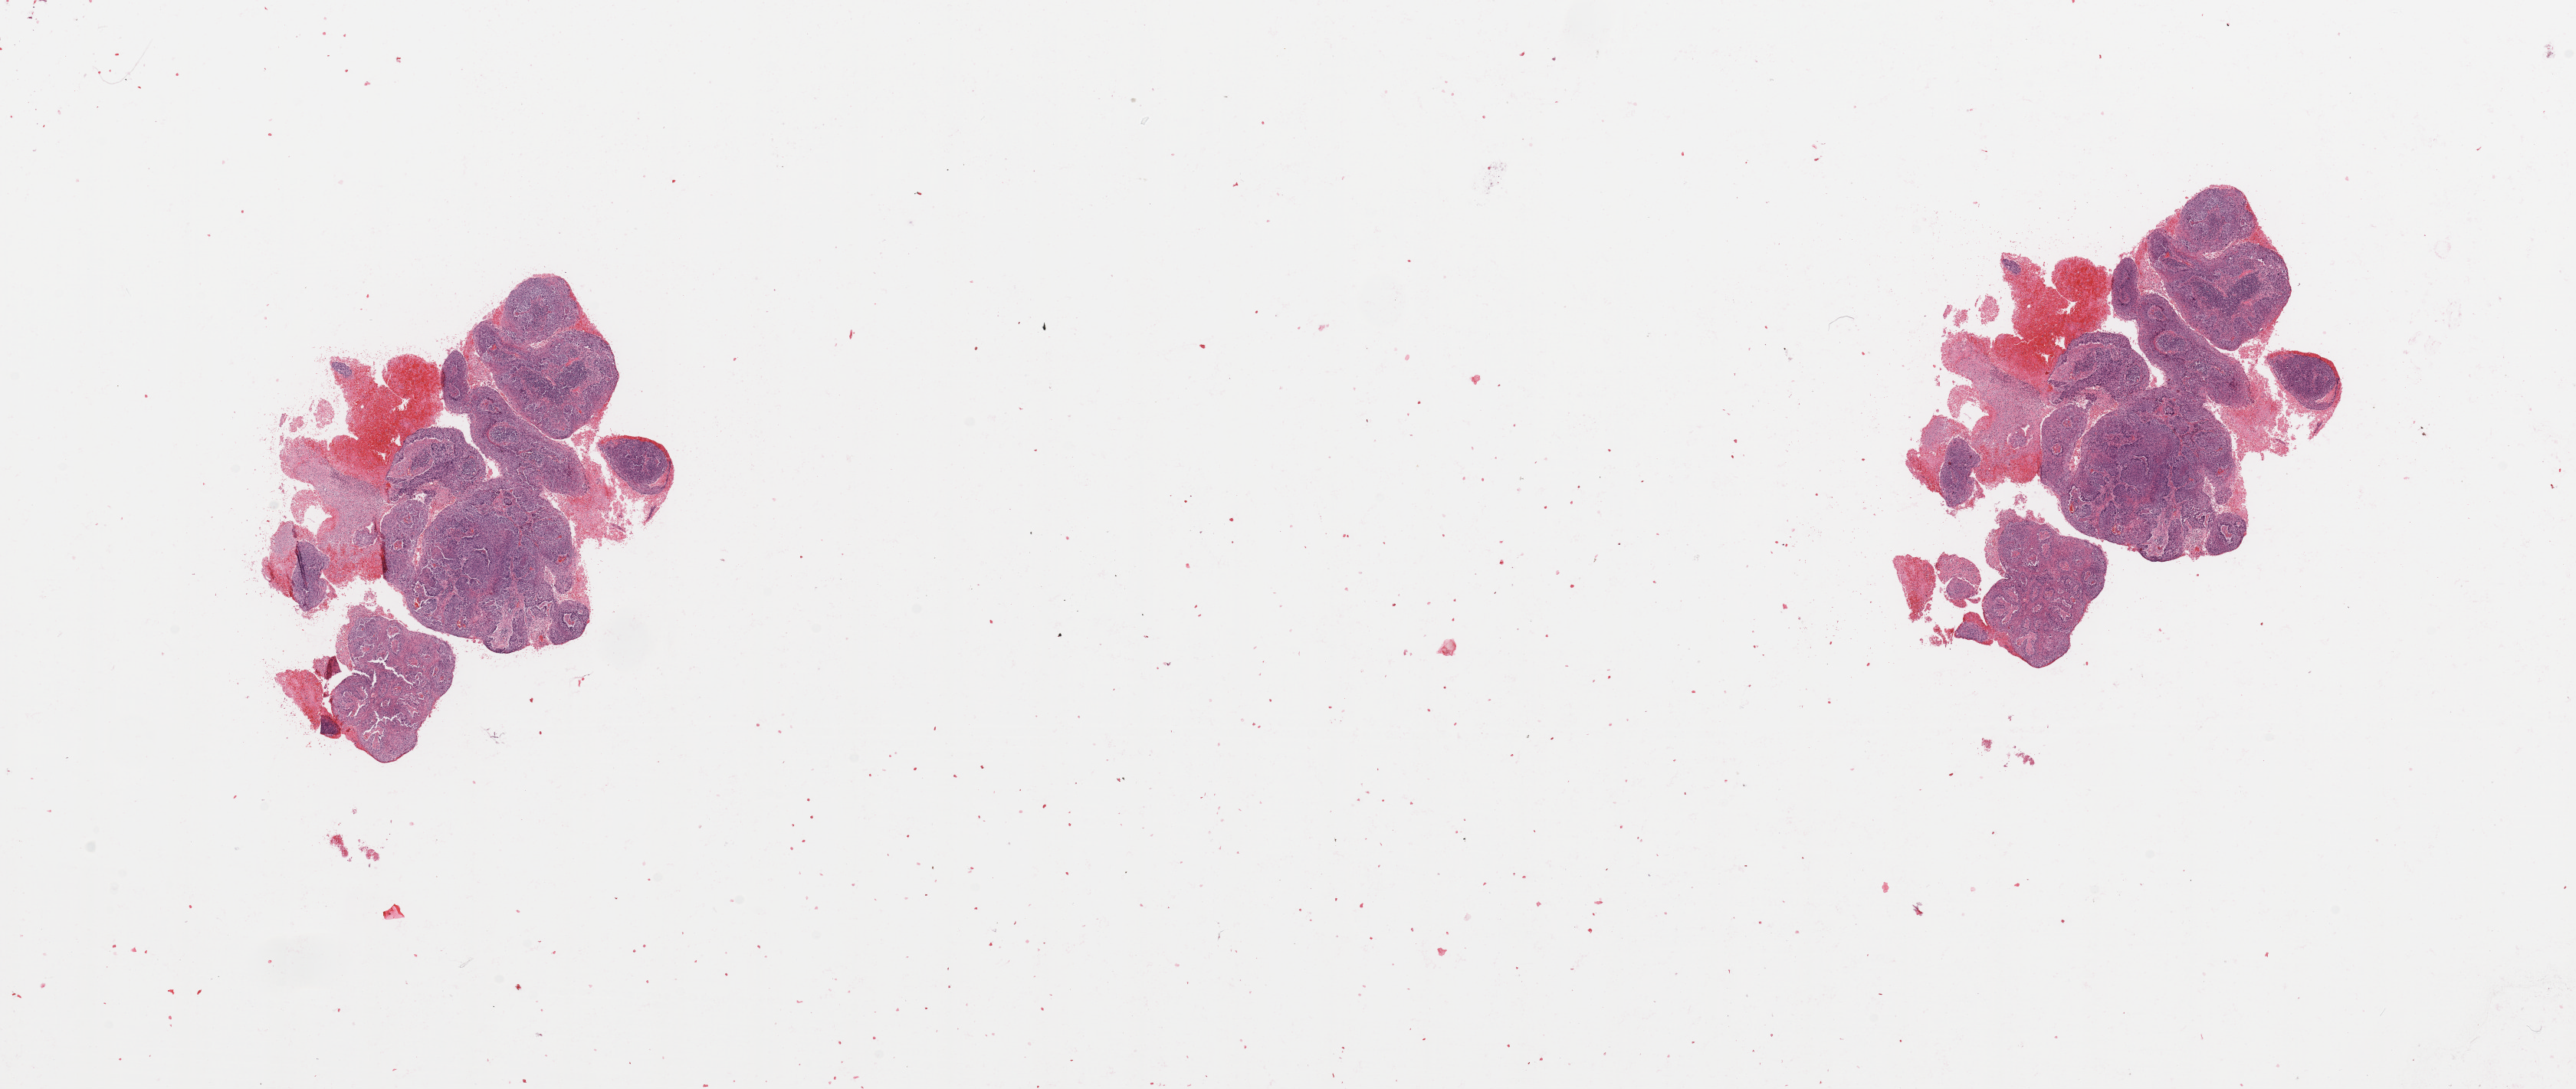
Whole-slide histology image, H&E-stained — shown as a low-resolution overview of the whole scanned area (about 26.6 x 11.2 mm, from a 20x scan). Lung, tumour tissue. Patient: male, age 74 years. Histologic grade: G2 (moderately differentiated).
- primary tumour site (as recorded): right upper lobe
- AJCC pathologic stage: IB
- diagnosis: Squamous cell carcinoma, NOS